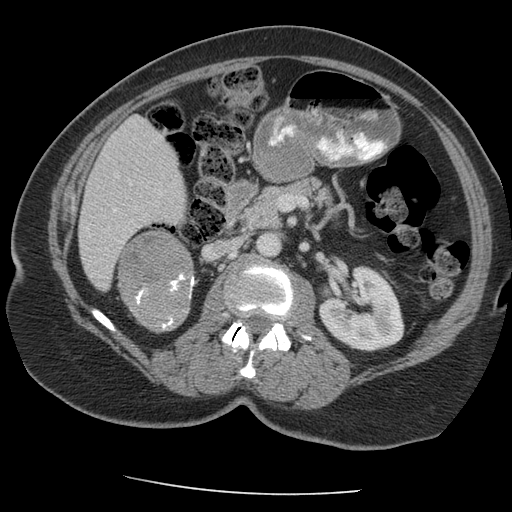
Contrast-enhanced abdominal CT, one axial slice; position 111 of 163 along the scan axis; reconstruction kernel STANDARD; 140 kVp; soft-tissue window (W 400 / L 40 HU); 2.5 mm slice thickness; 512 × 512 image matrix, field of view 360 × 360 mm. Patient: female, 70 years. Case-level facts recorded for this patient, not image findings: diagnosis: adrenocortical carcinoma; tumour side: right adrenal; tumour size at pathology: 9.5 cm; Ki-67 index: 5 %; stage (as recorded): 2.
Annotated regions visible in this slice (semi-automatically segmented with operator editing):
- mass: box from (x=121, y=232) to (x=193, y=331) px